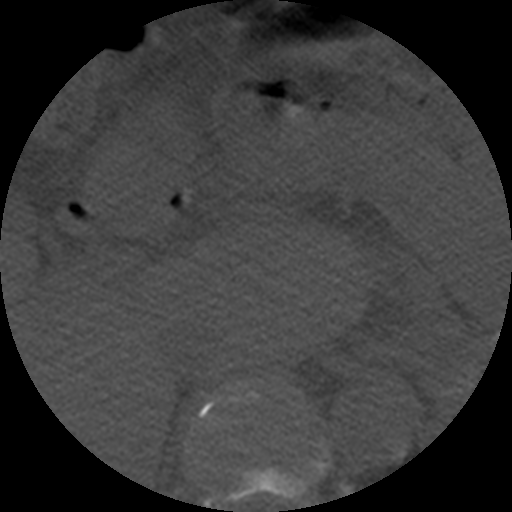
CT including the spine, one axial slice; slice 255 of 508 in the series (ordered by position); reconstruction kernel STANDARD; 120 kVp; bone window (W 1800 / L 400 HU); 512 × 512 image matrix, field of view 160 × 160 mm. Patient age 57 years. From the clinical record (not read from this slice): primary cancer: prostate.
Outlined on this slice (semi-automatically segmented with operator editing):
- T10 vertebra: bounding box <198,385,328,506> (left, top, right, bottom; pixels)
- T11 vertebra: <191,385,260,432>